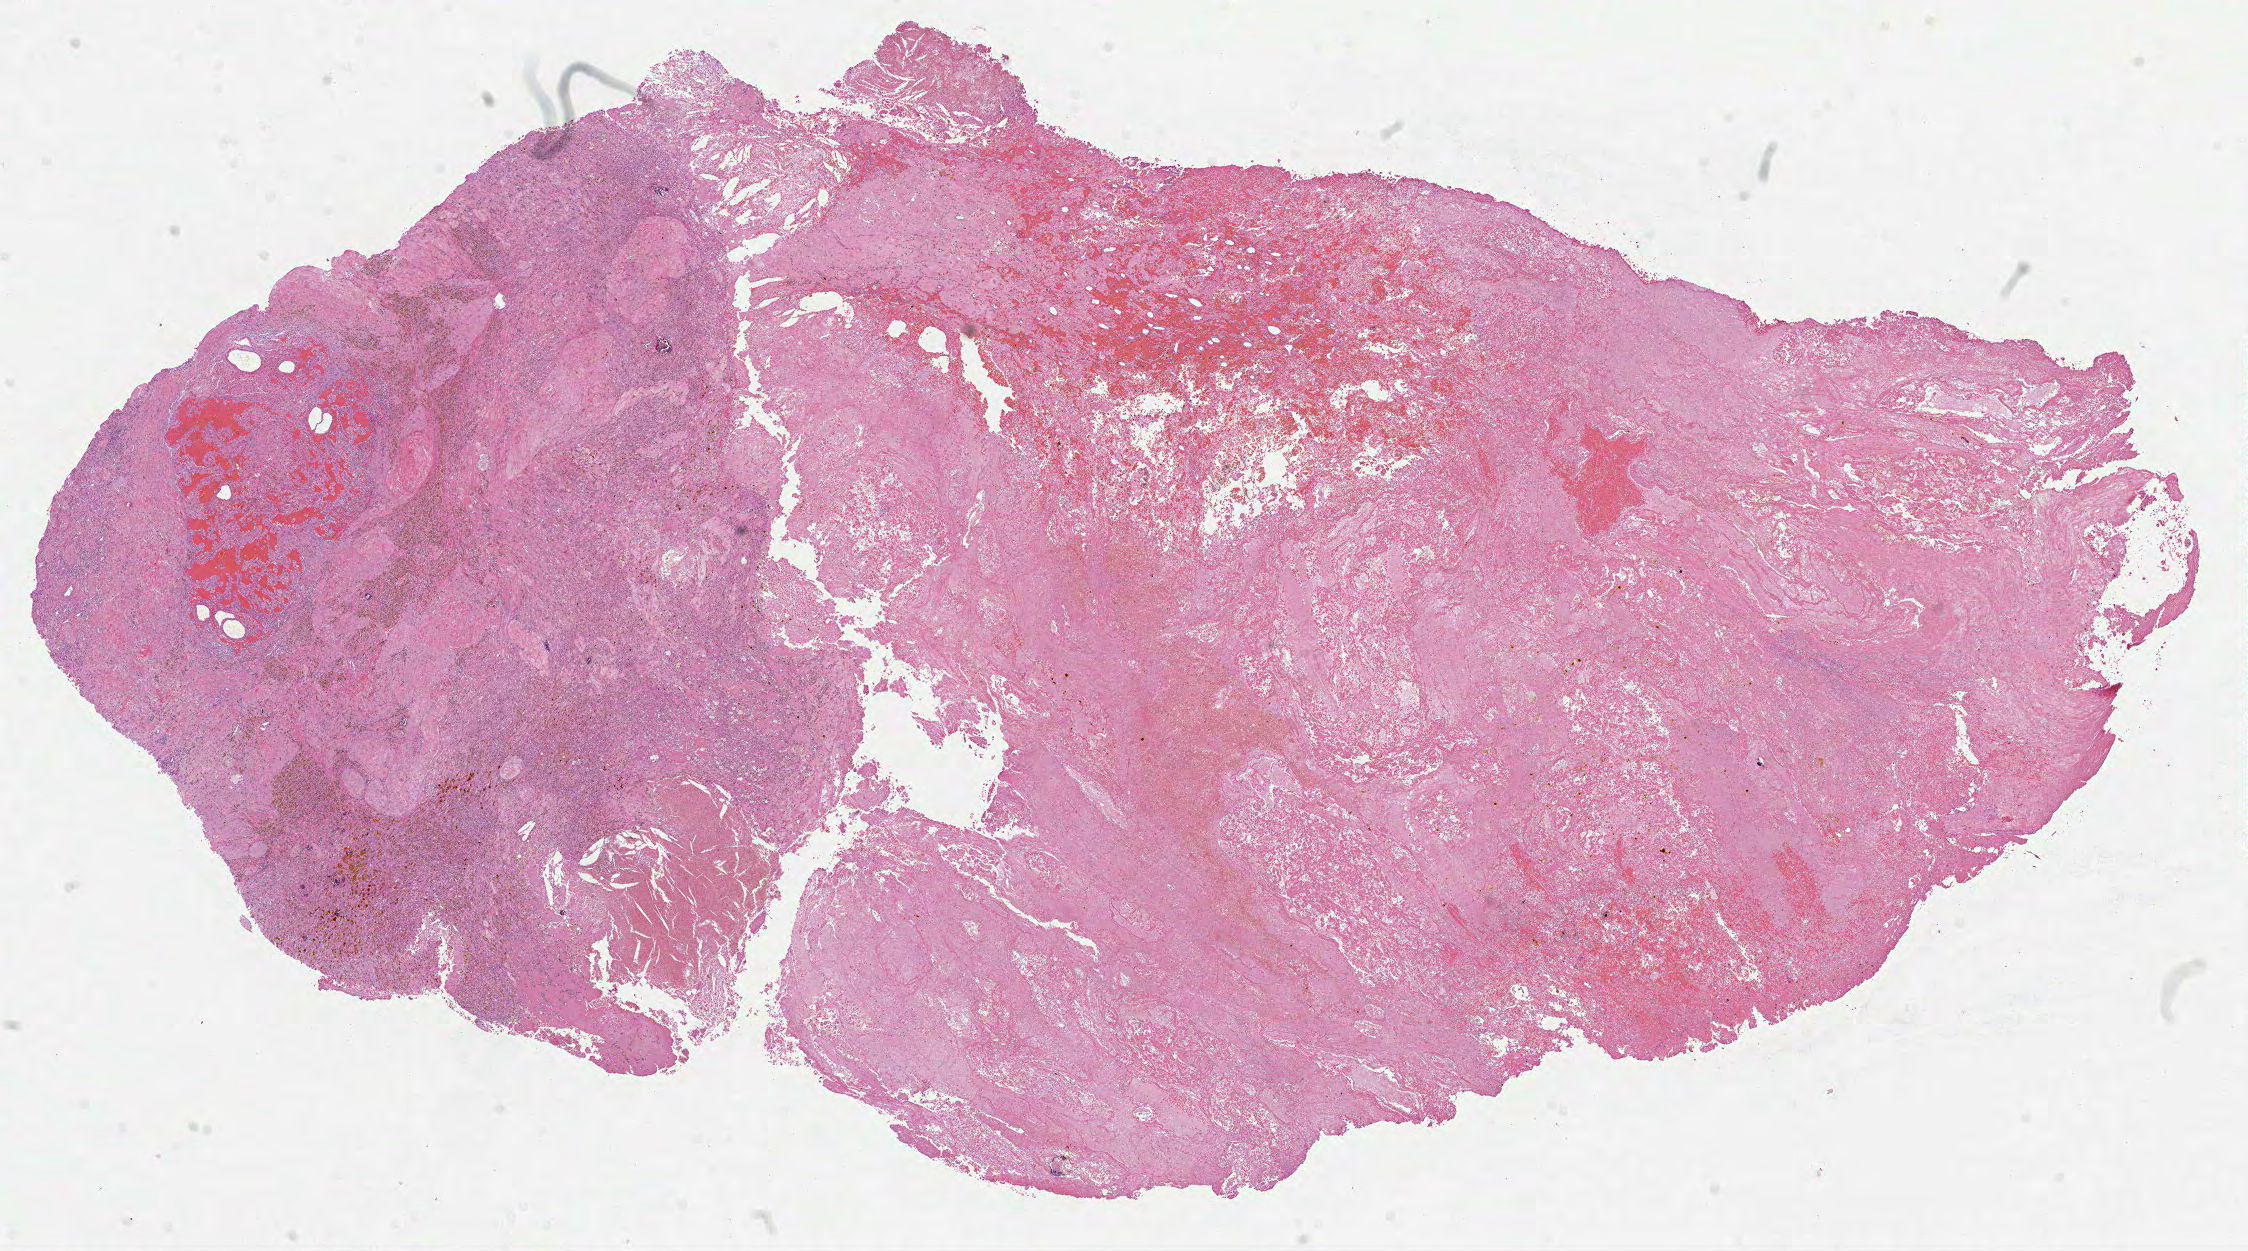
Whole-slide histology image, H&E-stained, shown as a low-resolution overview of the whole scanned area (about 18.1 x 10.1 mm, acquisition: 40x scan), formalin-fixed paraffin-embedded (FFPE) diagnostic section, primary tumour sample from the kidney. Male patient; age at initial diagnosis 67 years.
Histologic diagnosis: Papillary adenocarcinoma, NOS.